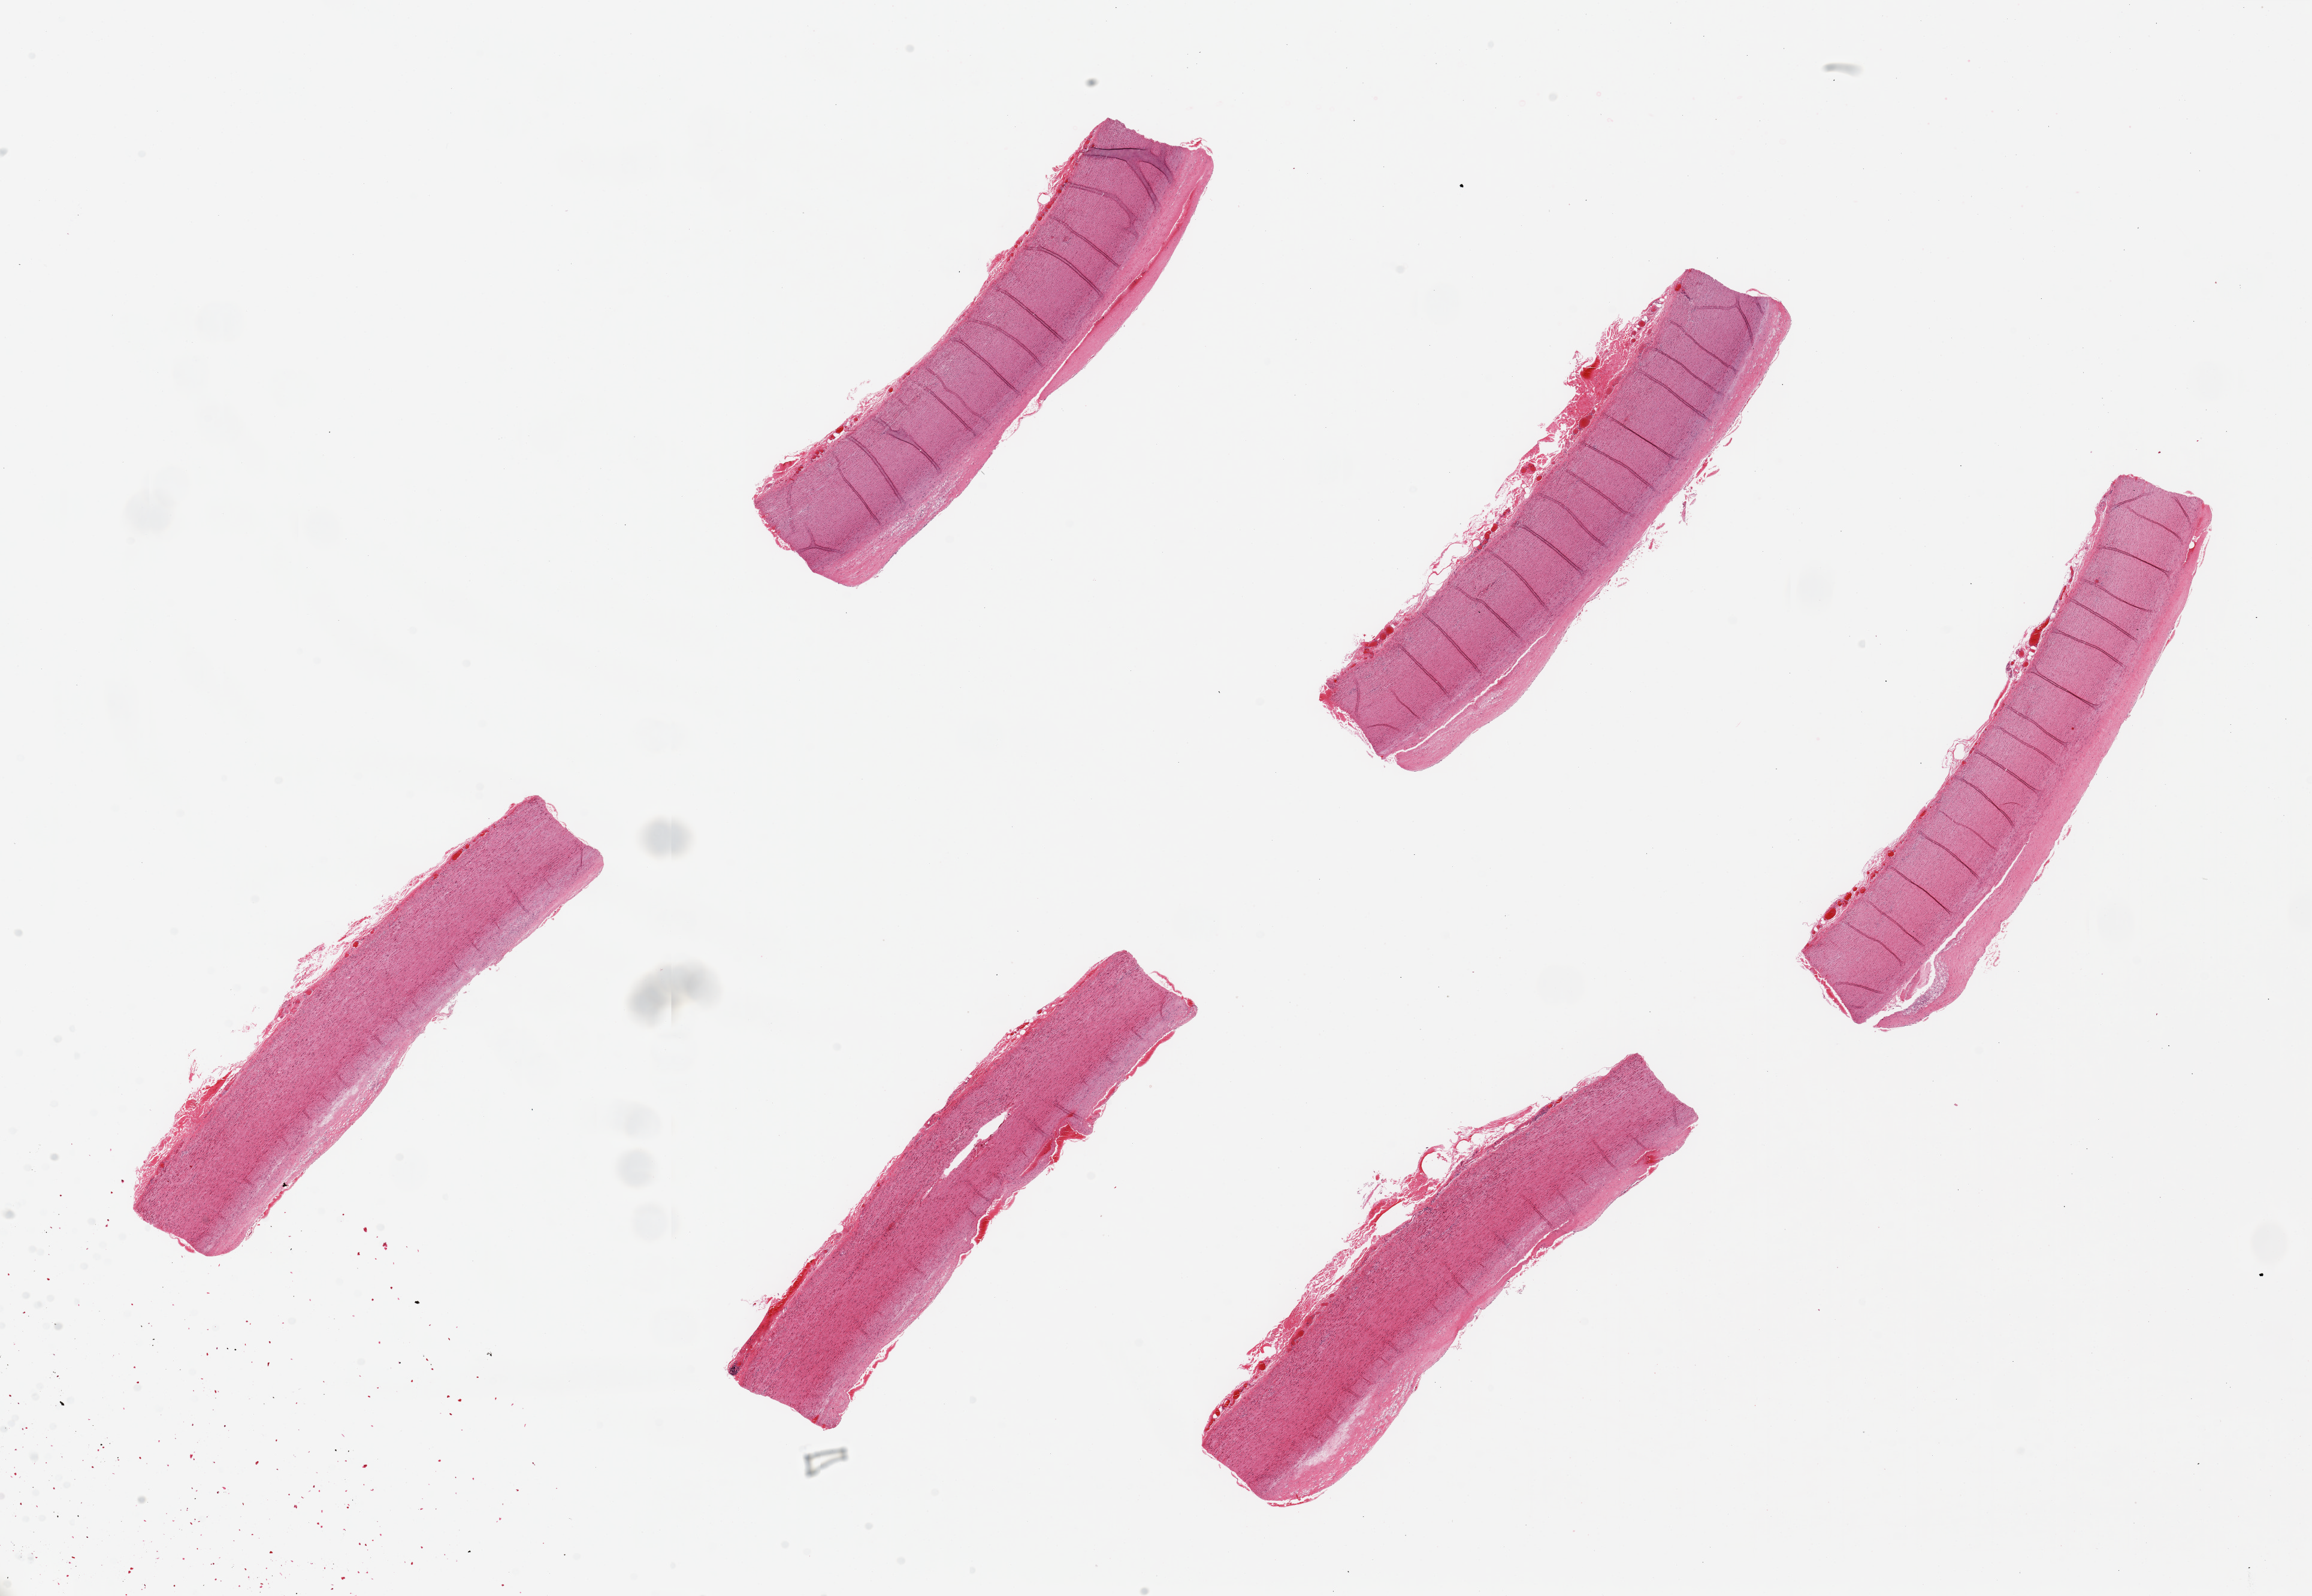
Whole-slide image, H&E stain — shown as a low-resolution overview of the whole scanned area (about 30.5 x 21.1 mm, from a 20x scan), PAXgene-fixed, paraffin-embedded tissue, section of aorta (target tissue), donor tissue sample. Donor: male.
• review note (as recorded): 6 pieces ~8x1.5mm; Up to ~0.25mm layer atherosis present